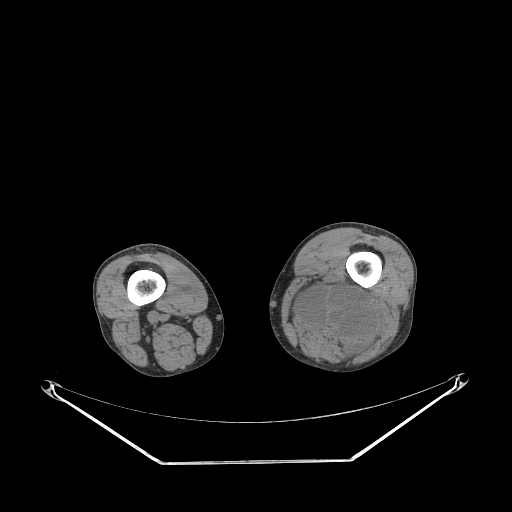
CT of an extremity soft-tissue mass (from a PET/CT study), one axial slice; 140 kVp; soft-tissue window (W 400 / L 40 HU); 512 × 512 image matrix, field of view 500 × 500 mm. Male patient. Case-level facts recorded for this patient, not image findings: histological type: undifferentiated pleomorphic liposarcoma; grade: high; site of the primary tumour: left thigh.
Structures marked on this image (expert contour drawn on MRI and transferred to this co-registered scan by the dataset authors):
- gross tumour volume including surrounding oedema: bounding box <290,276,378,357> (left, top, right, bottom; pixels)
- gross tumour volume (mass): <299,290,368,341>